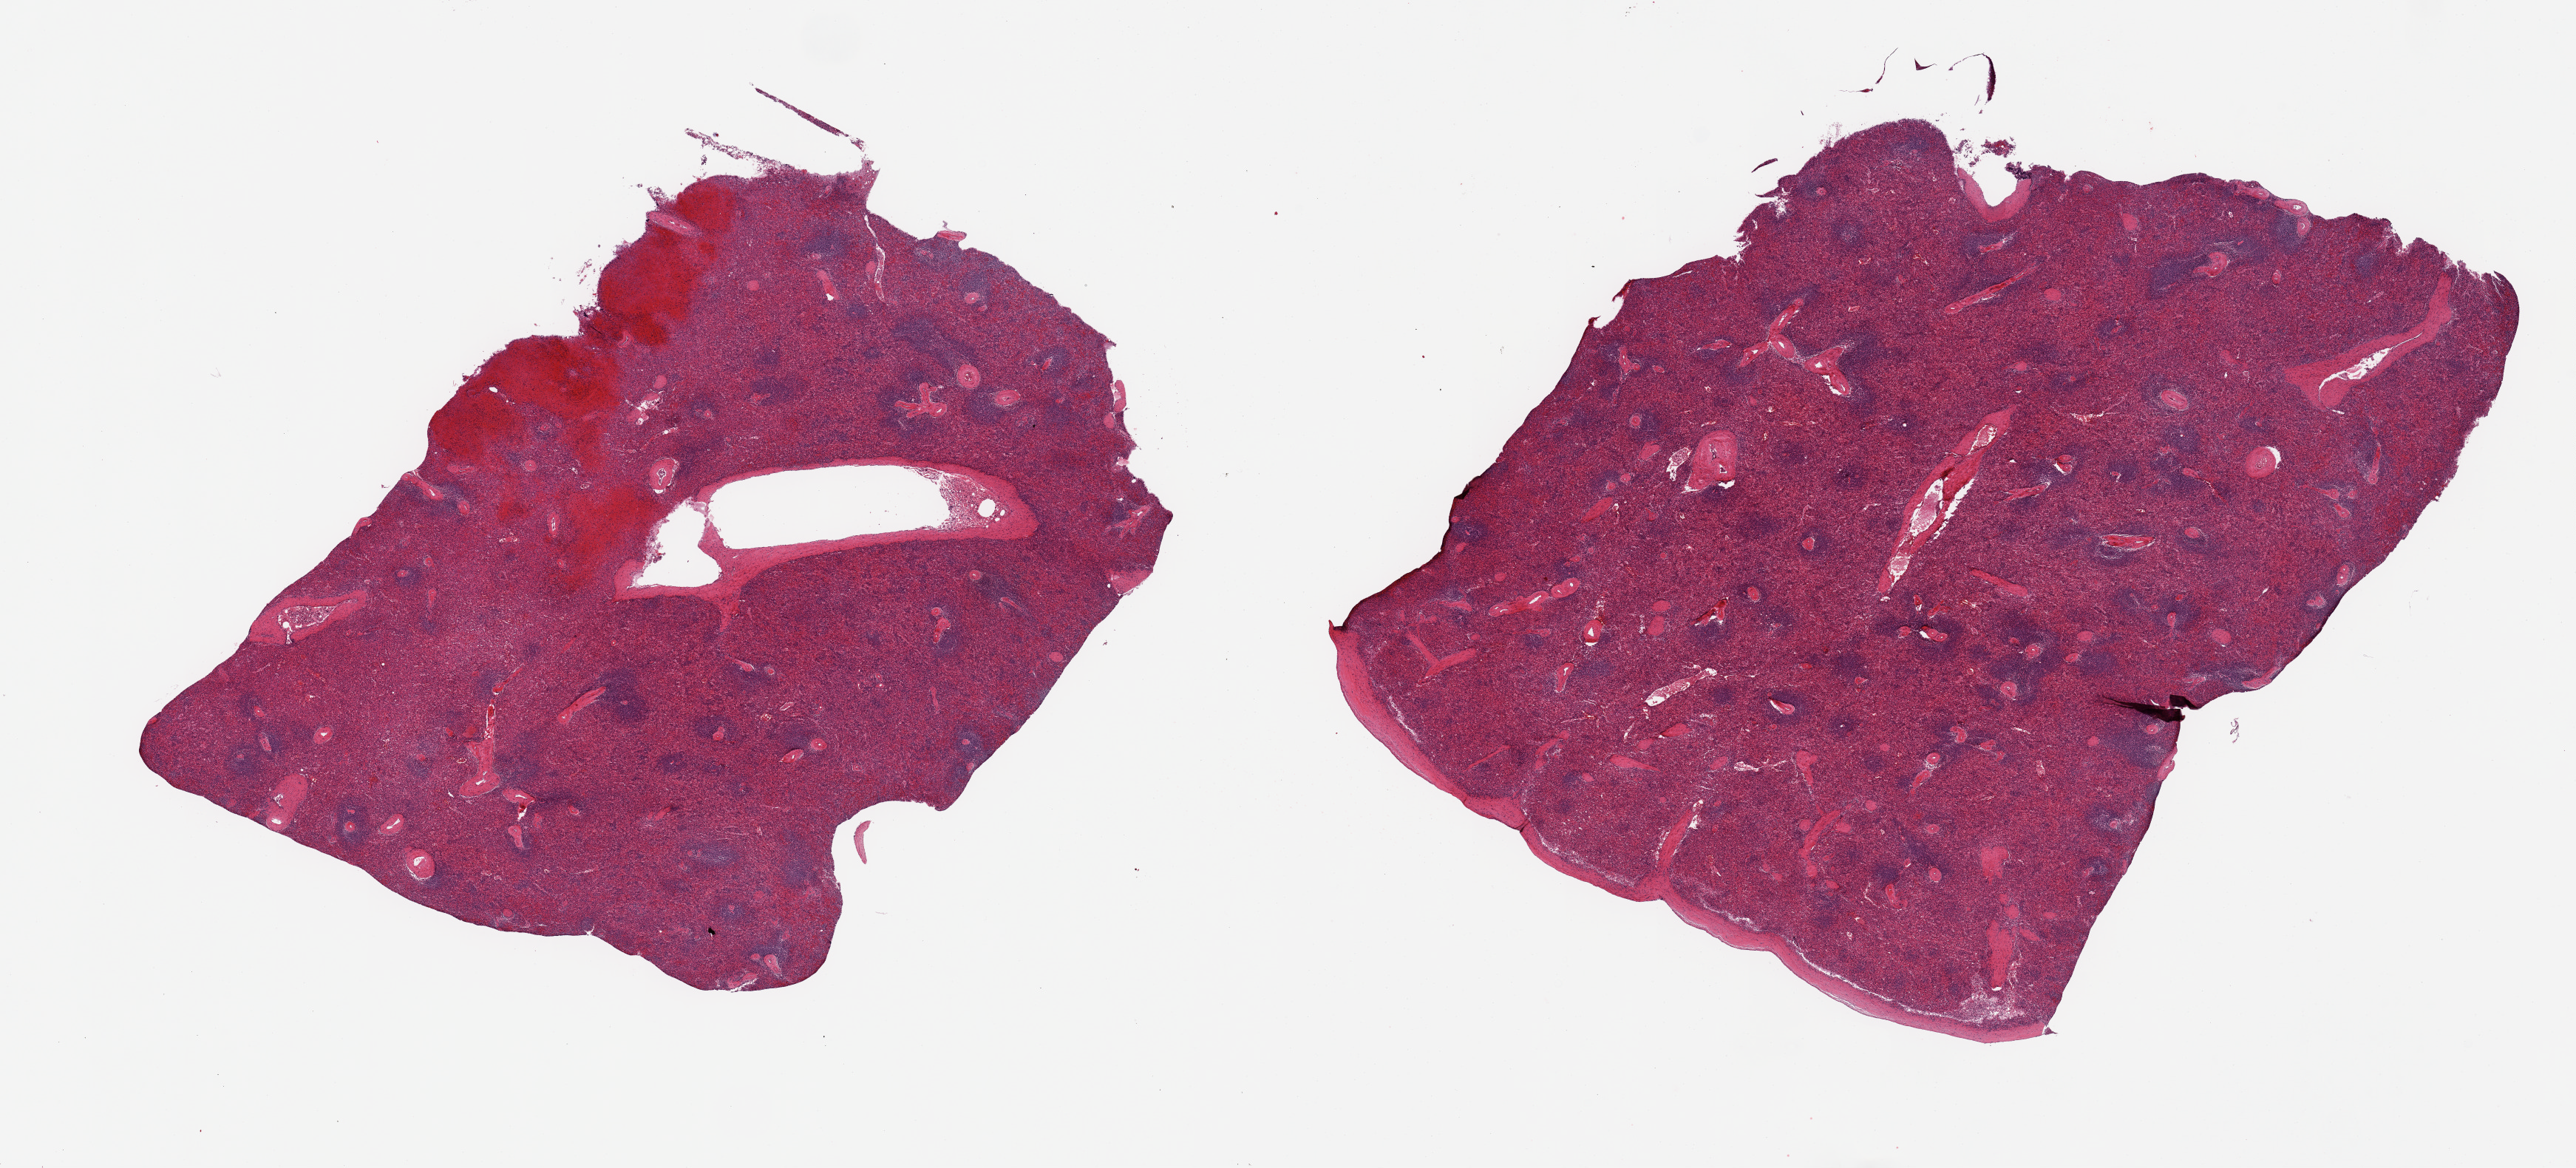
H&E whole-slide image, a low-resolution overview of the entire scanned area, about 27.6 x 12.5 mm. PAXgene-fixed, paraffin-embedded tissue. Target tissue: spleen. Tissue donor sample. Male donor.
Reviewer comment on this tissue sample: 2 pieces, no abnormalities.